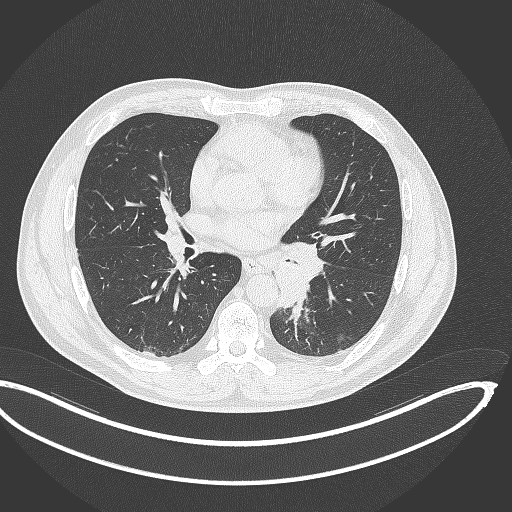
Chest CT, one axial slice; position 178 of 362 along the scan axis; 120 kVp; lung window (W 1500 / L -600 HU); 512 × 512 image matrix, field of view 442 × 442 mm. Patient: male, 50 years. From the clinical record (not read from this slice): clinical TNM (as recorded): T2a N3 M0.
Outlined on this slice (rectangle marked by the reading radiologist):
- lung tumour (recorded histology: squamous cell carcinoma): bounding box [x1, y1, x2, y2] px = [273, 236, 326, 314]